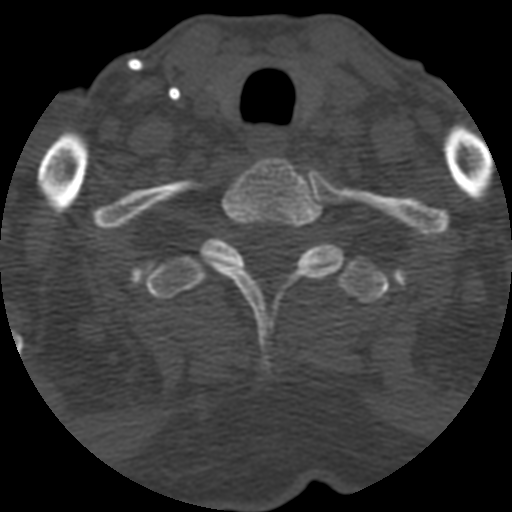
CT including the spine, one axial slice. Slice 513 of 708 in the series (ordered by position). Reconstruction kernel STANDARD. 120 kVp. One of 3 acquisitions stored at this slice position. Bone window (W 1800 / L 400 HU). 512 × 512 image matrix, field of view 160 × 160 mm. Patient age 55 years. From the clinical record (not read from this slice): primary cancer: colon; vertebrae with lytic lesions (as recorded): T12, L1, L5.
Structures marked on this image (semi-automatic segmentation, software-assisted and operator-edited):
- T1 vertebra: bounding box <200,158,345,343> (left, top, right, bottom; pixels)
- T2 vertebra: <145,238,389,303>